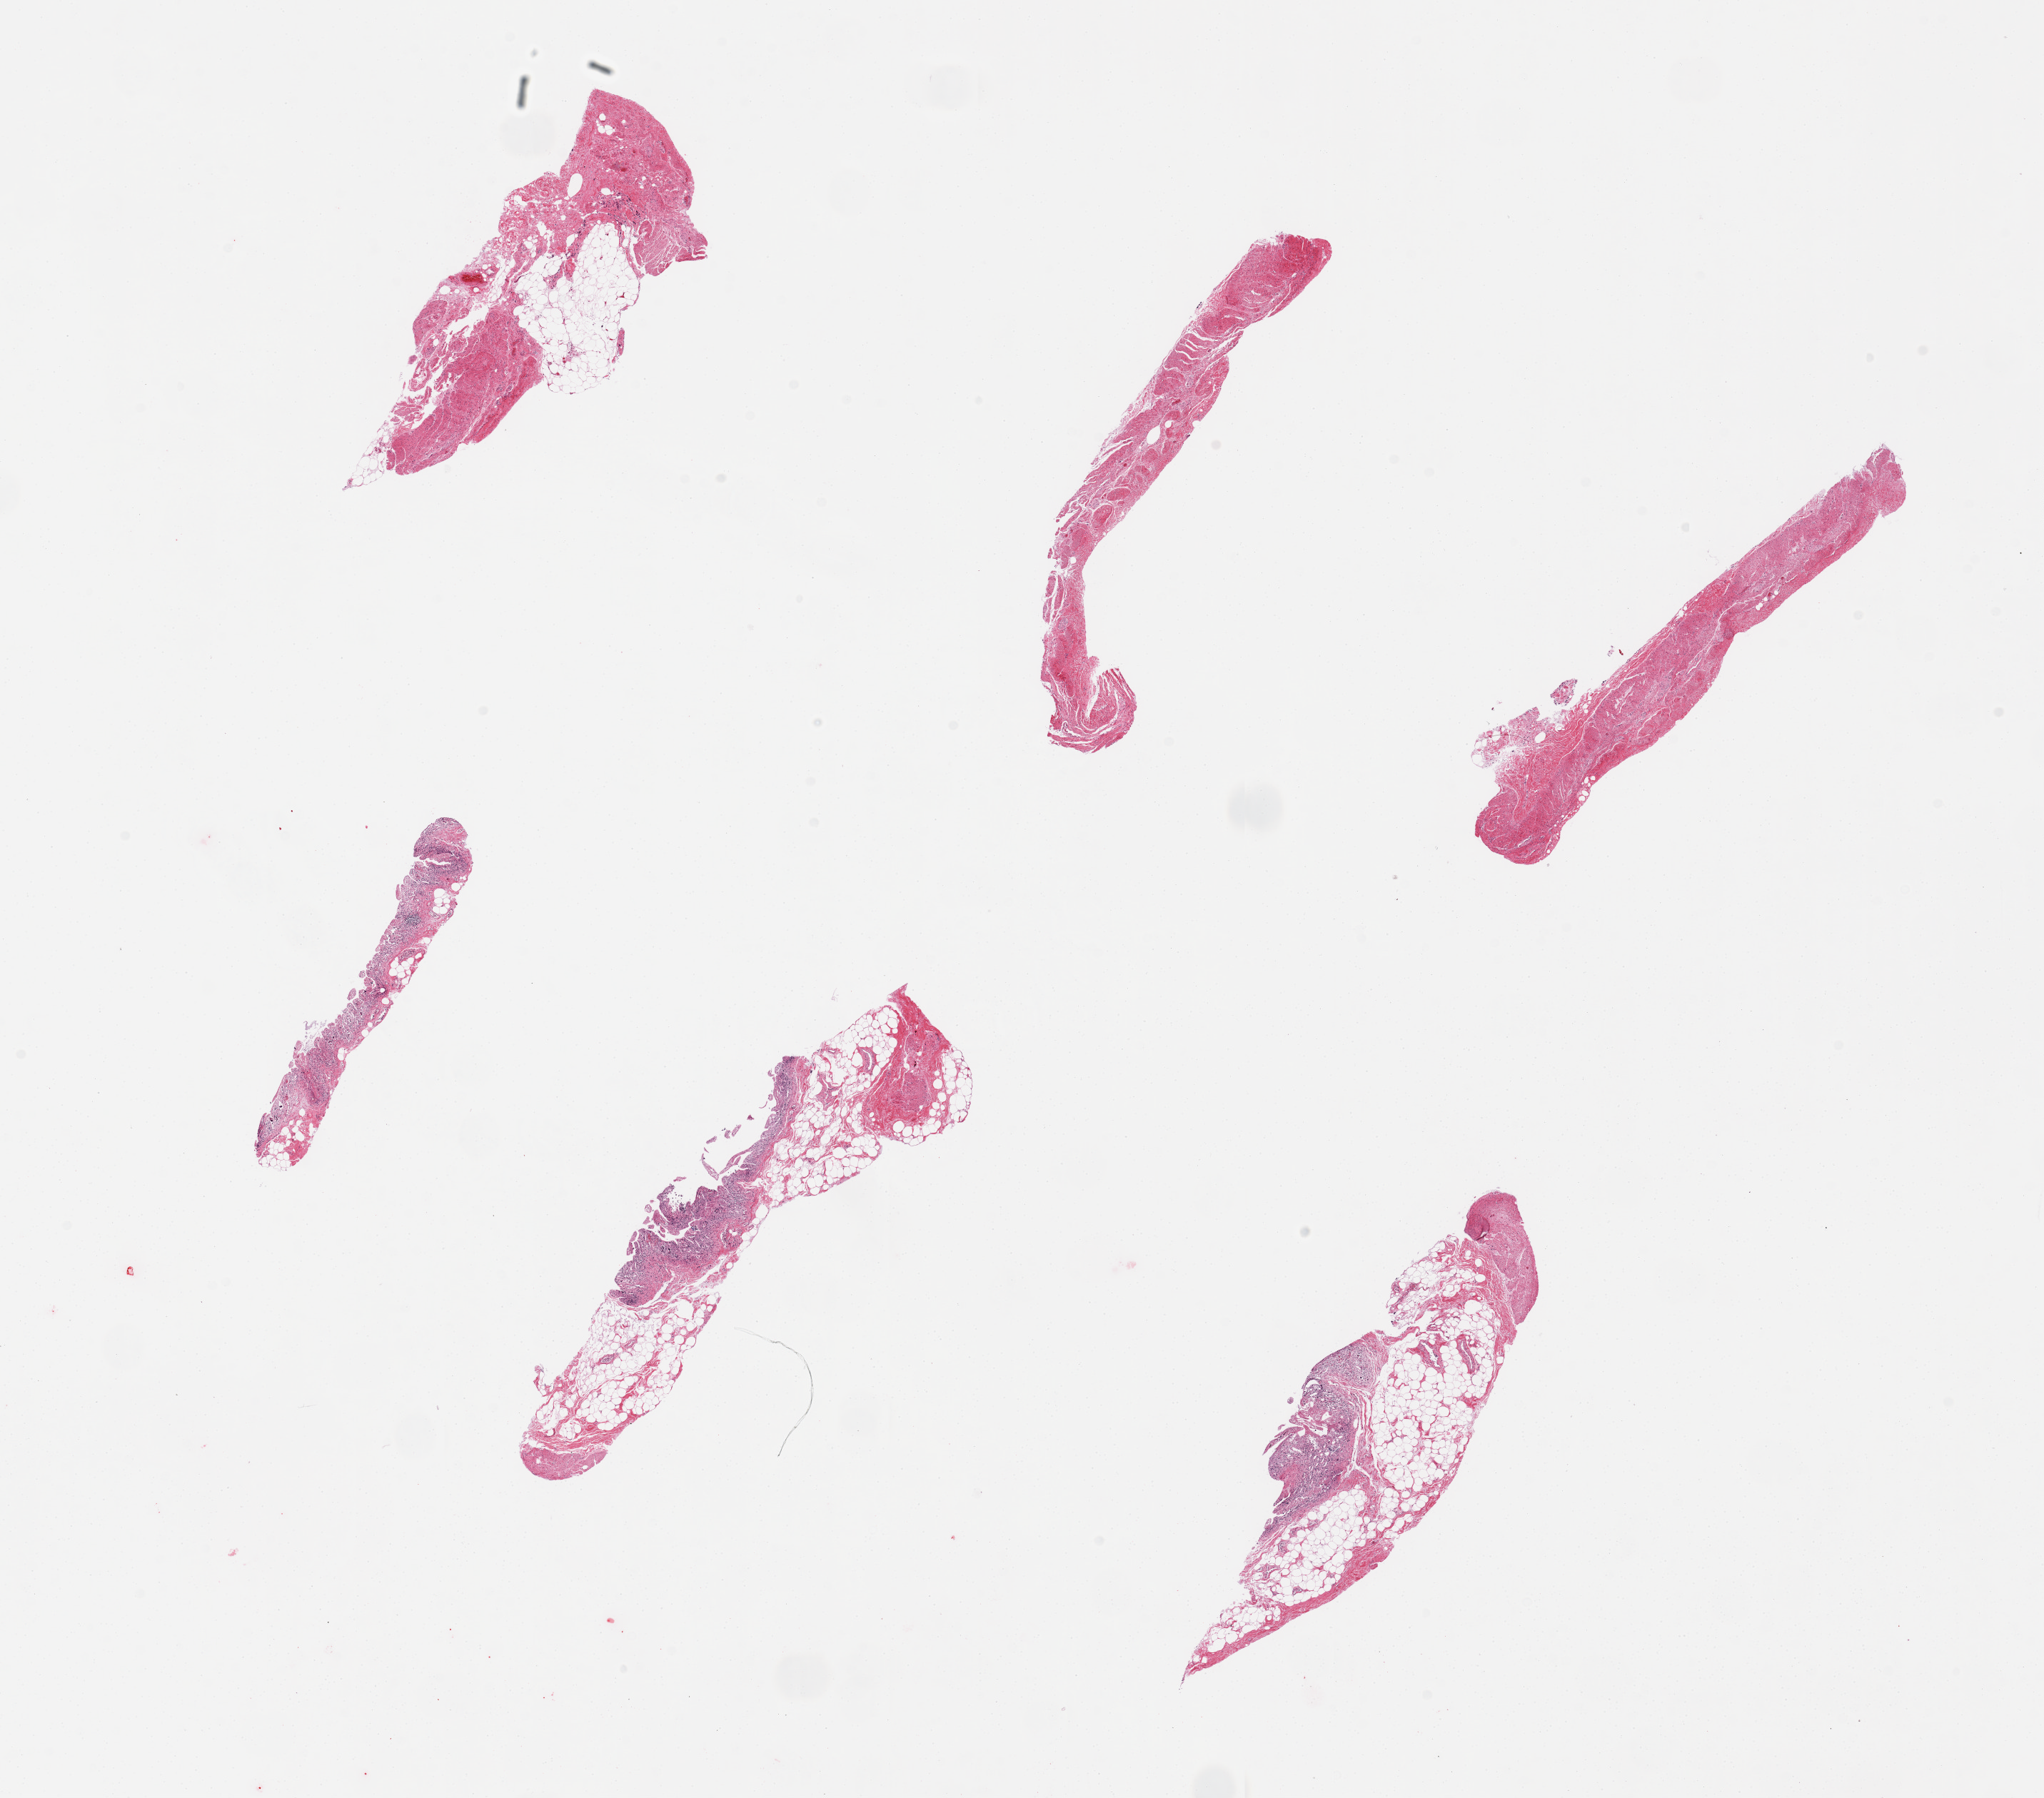
Whole-slide image, haematoxylin and eosin stain, brightfield — whole scanned area (about 22.6 x 19.9 mm) shown as a low-resolution overview, PAXgene-fixed paraffin-embedded (PFPE) section, section of ileum (target tissue), tissue donor sample. Male donor.
- reviewer comment on this tissue sample: 6 pieces; mucosa completely autolyzed; insufficient lymphoid tissue